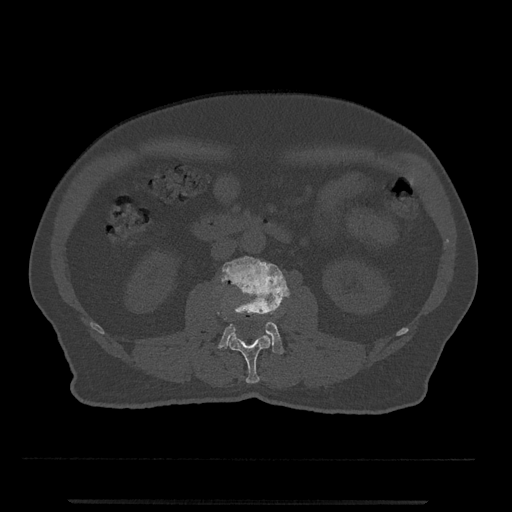
CT including the spine, one axial slice. Position 237 of 797 along the scan axis. 120 kVp. Bone window (W 1800 / L 400 HU). 512 × 512 image matrix, field of view 419 × 419 mm. Male patient, age 63 years. Case-level facts recorded for this patient, not image findings: primary cancer: prostate.
Structures marked on this image (semi-automatically segmented with operator editing):
- L2 vertebra: bounding box (x1, y1, x2, y2) in pixels: (217, 292, 273, 383)
- L3 vertebra: (218, 256, 290, 354)